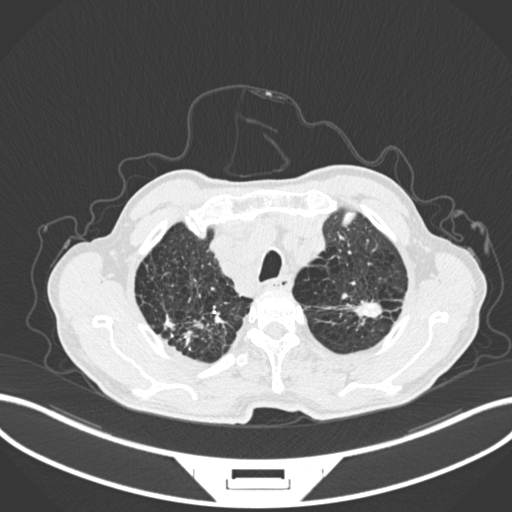
Chest CT, one axial slice; position 235 of 287 along the scan axis; reconstruction kernel B30f; lung window (W 1500 / L -600 HU); 1 mm slice thickness; 512 × 512 image matrix, field of view 400 × 400 mm. Male patient, age 74 years. From the clinical record (not read from this slice): clinical TNM (as recorded): T2a N1 M0.
Structures marked on this image (bounding box drawn by a radiologist):
- lung tumour (recorded histology: adenocarcinoma): bounding box [x1, y1, x2, y2] px = [347, 299, 386, 321]